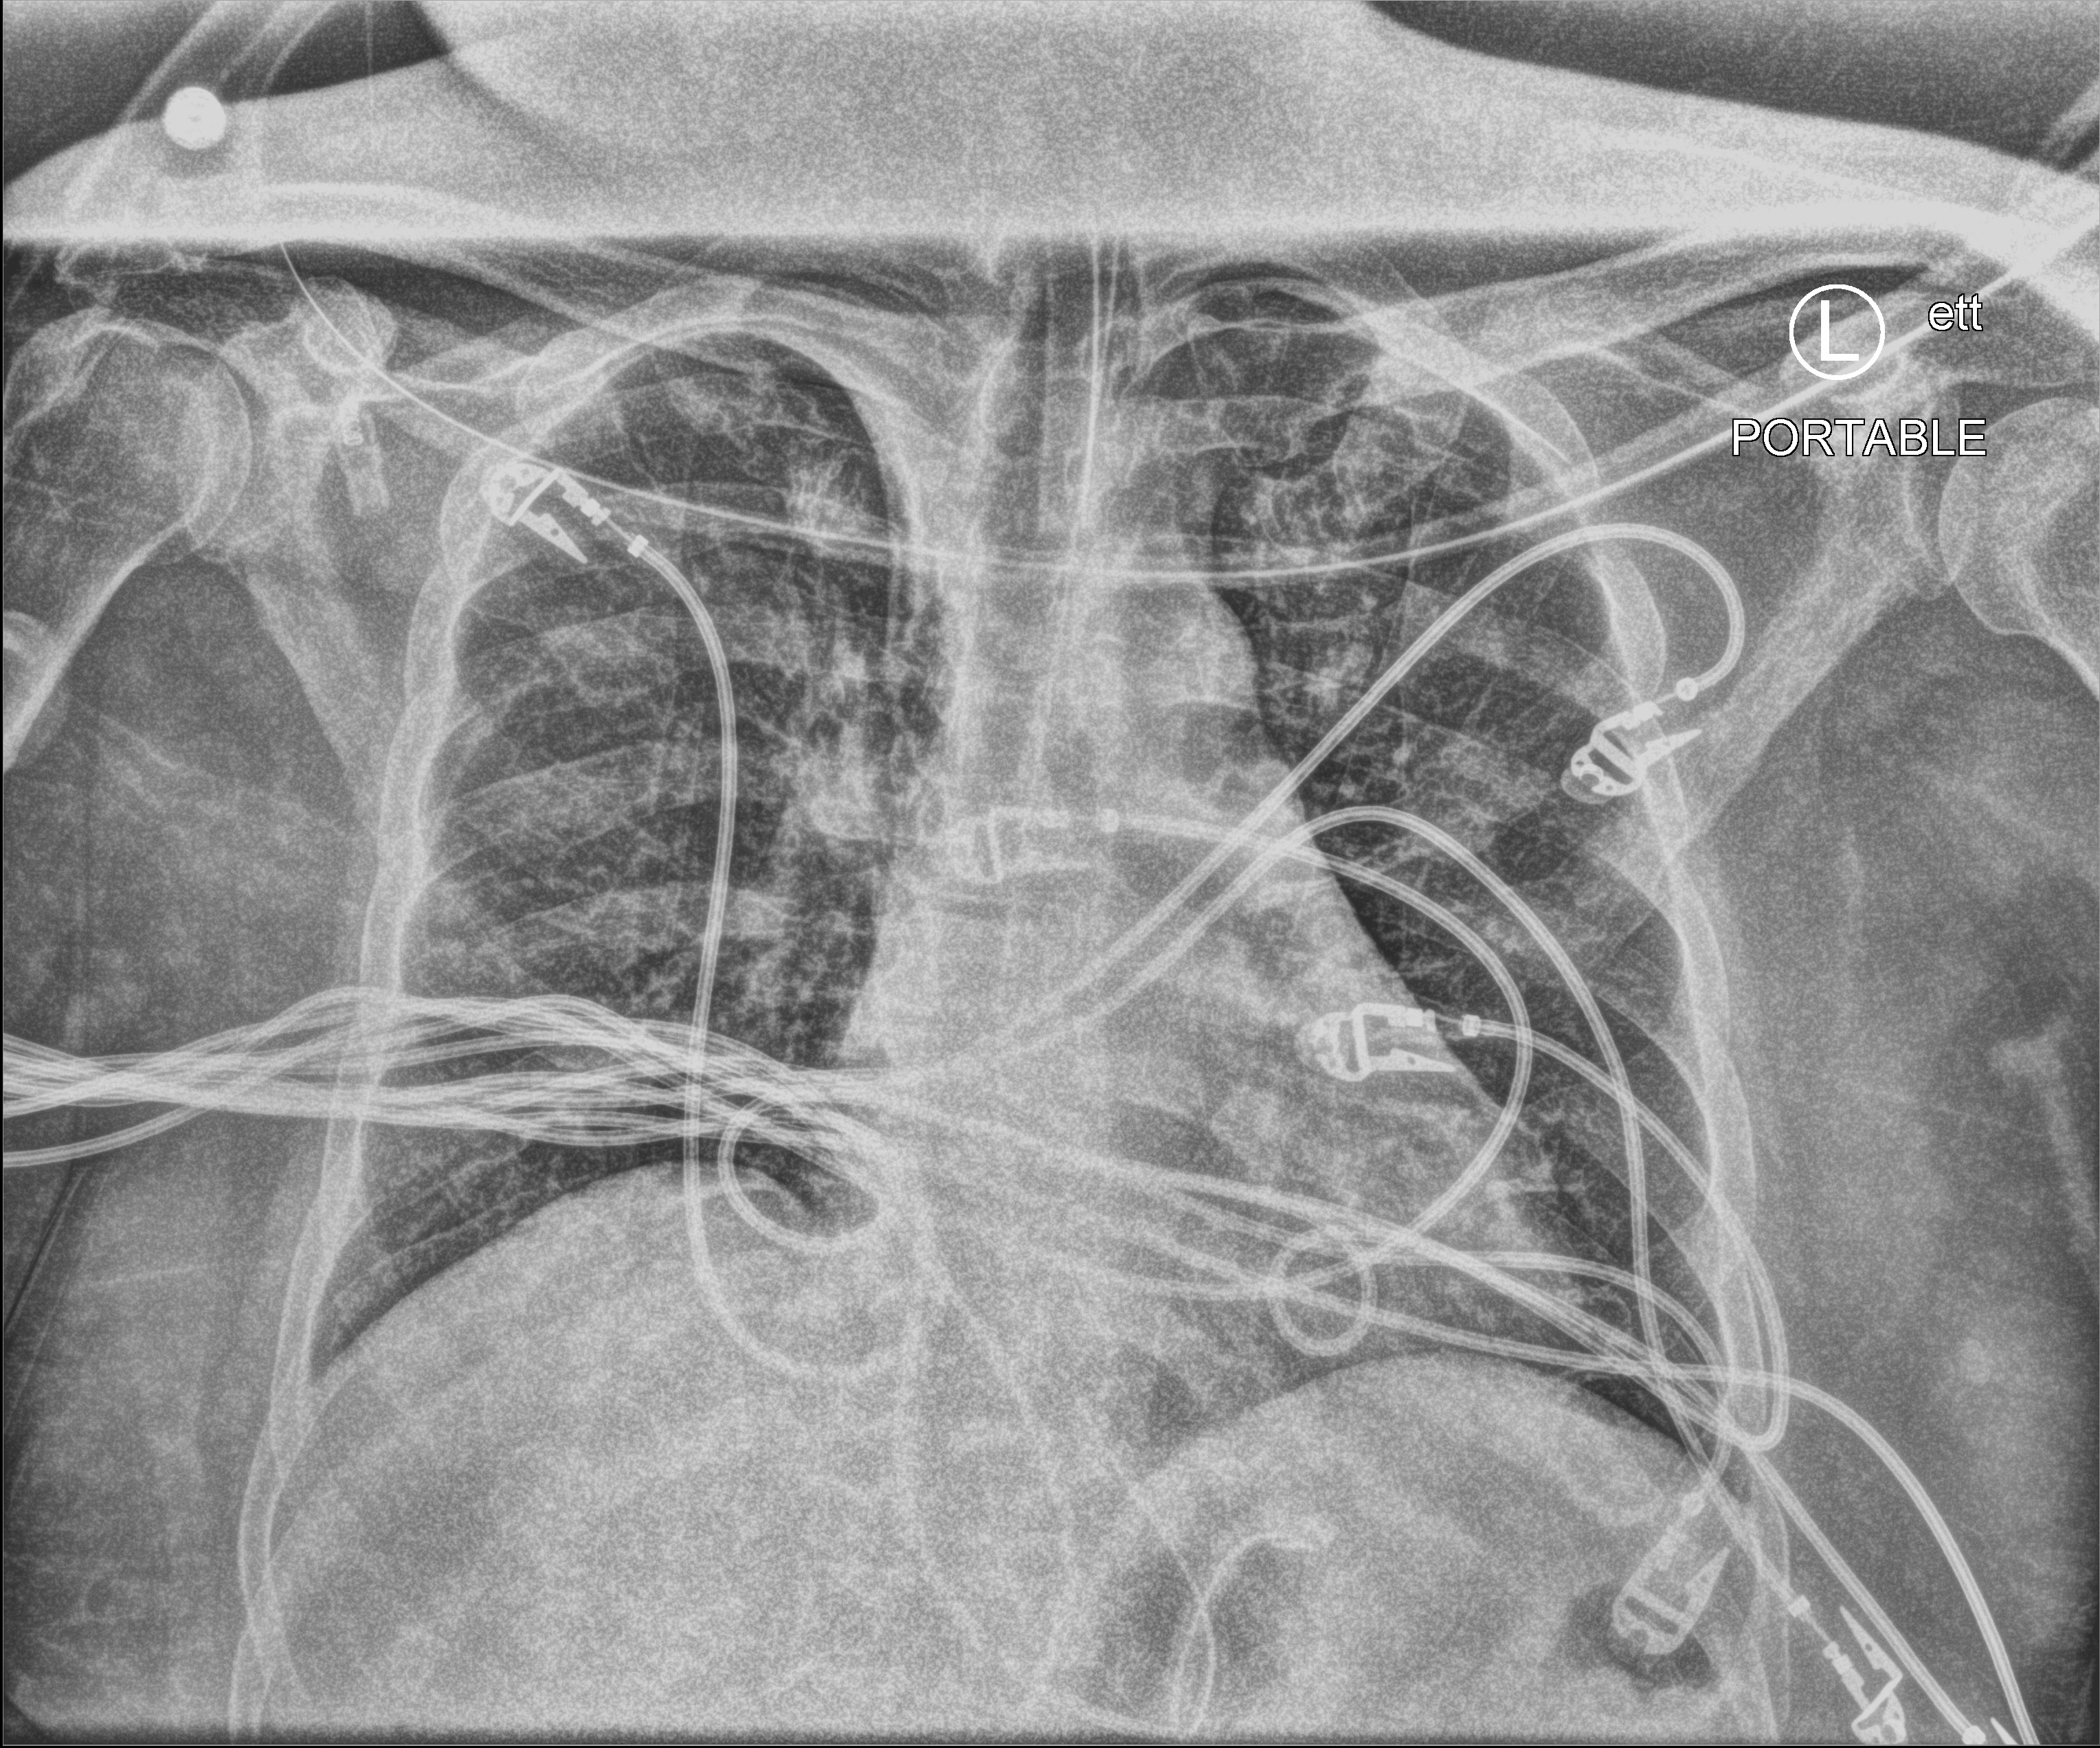
Chest X-ray (portable). Adult patient hospitalised with COVID-19, age 18–59 years.
From the hospital-stay record, not from the radiograph (when in the stay this image was taken is not recorded): mechanically ventilated during this hospital stay: yes; length of hospital stay: 37 days; admitted to intensive care during this hospital stay: yes.